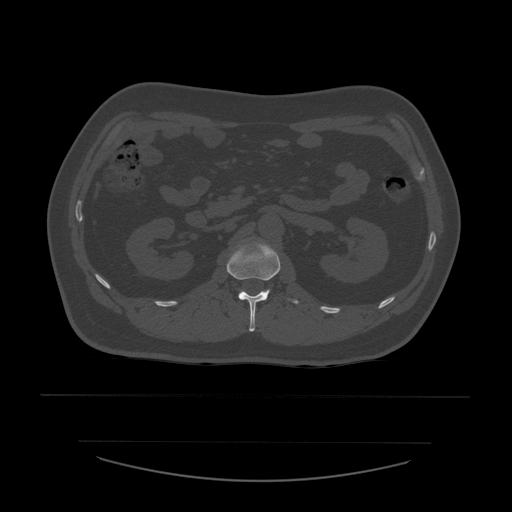
CT including the spine, one axial slice. Slice 221 of 532 in the series (ordered by position). Reconstruction kernel STANDARD. 120 kVp. Bone window (W 1800 / L 400 HU). 1.25 mm slice thickness. 512 × 512 image matrix, field of view 441 × 441 mm. Patient age 44 years. Case-level facts recorded for this patient, not image findings: primary cancer: soft tissue sarcoma.
Outlined on this slice (semi-automatically segmented with operator editing):
- L1 vertebra: box from (x=227, y=242) to (x=299, y=332) px